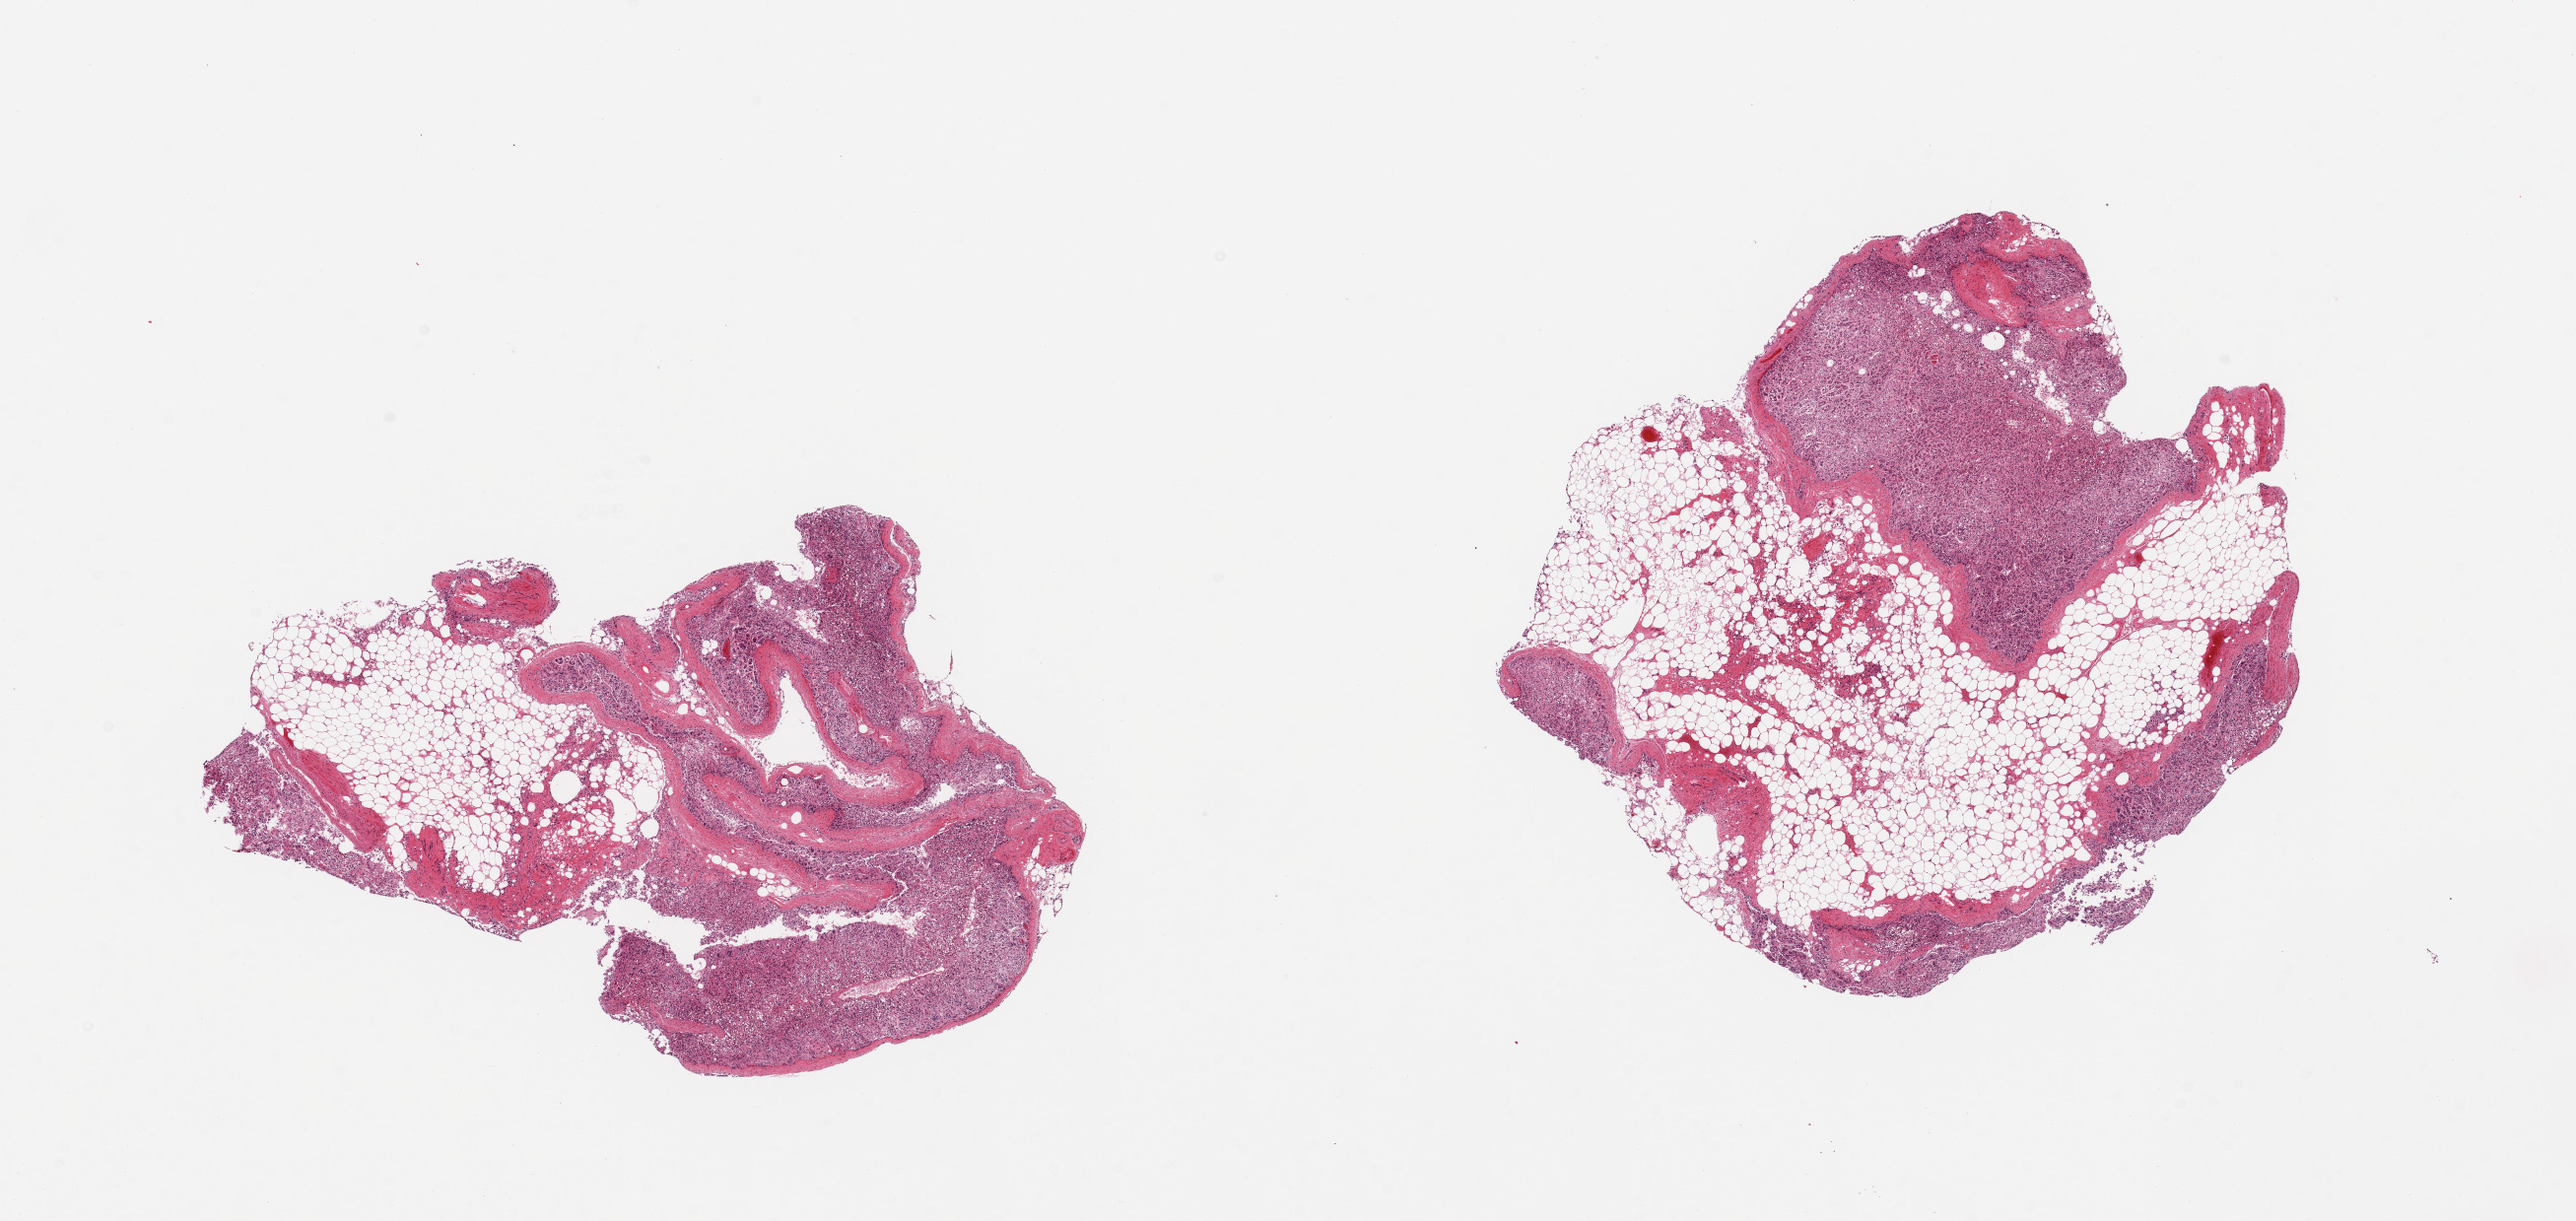
Whole-slide image, H&E stain — low-resolution overview of the scanned area, about 20.7 x 9.8 mm (from a 20x scan), PAXgene-fixed paraffin-embedded (PFPE) section, section of adrenal gland (target tissue), donor tissue sample. Male donor.
Review note (as recorded): 2 pieces; 50 and 60% attached and internal fat.